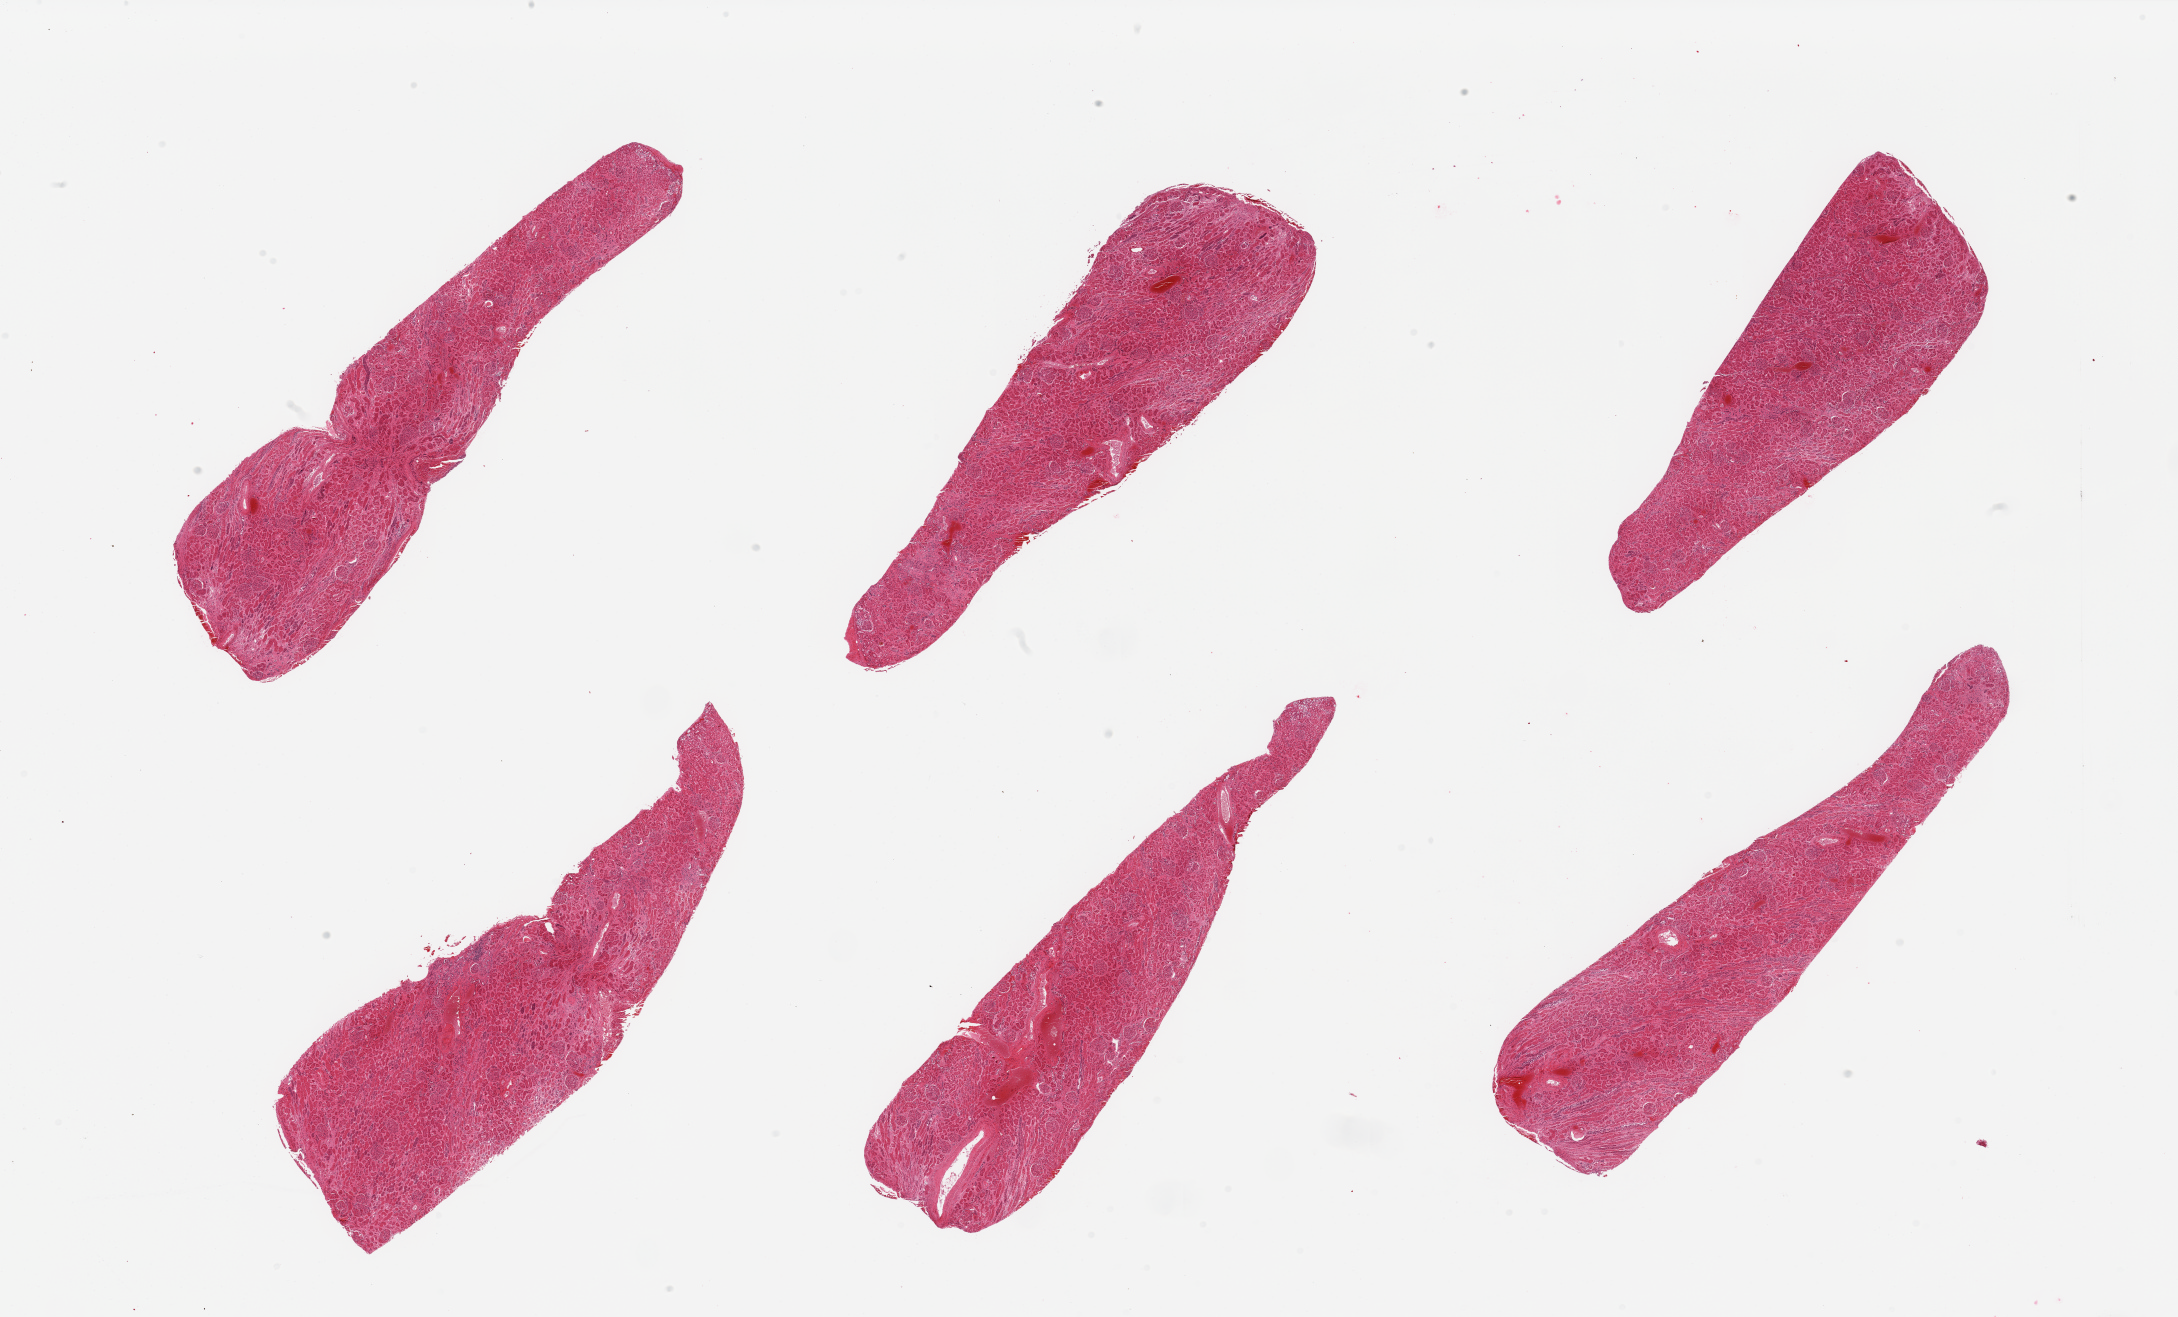
Whole-slide image, haematoxylin and eosin stain, whole scanned area (about 34.5 x 20.8 mm) shown as a low-resolution overview; PAXgene-fixed paraffin-embedded (PFPE) section; target tissue: renal cortex; donor tissue sample. Male donor.
Review note (as recorded): 6 pieces; no acute or chronic lesions.